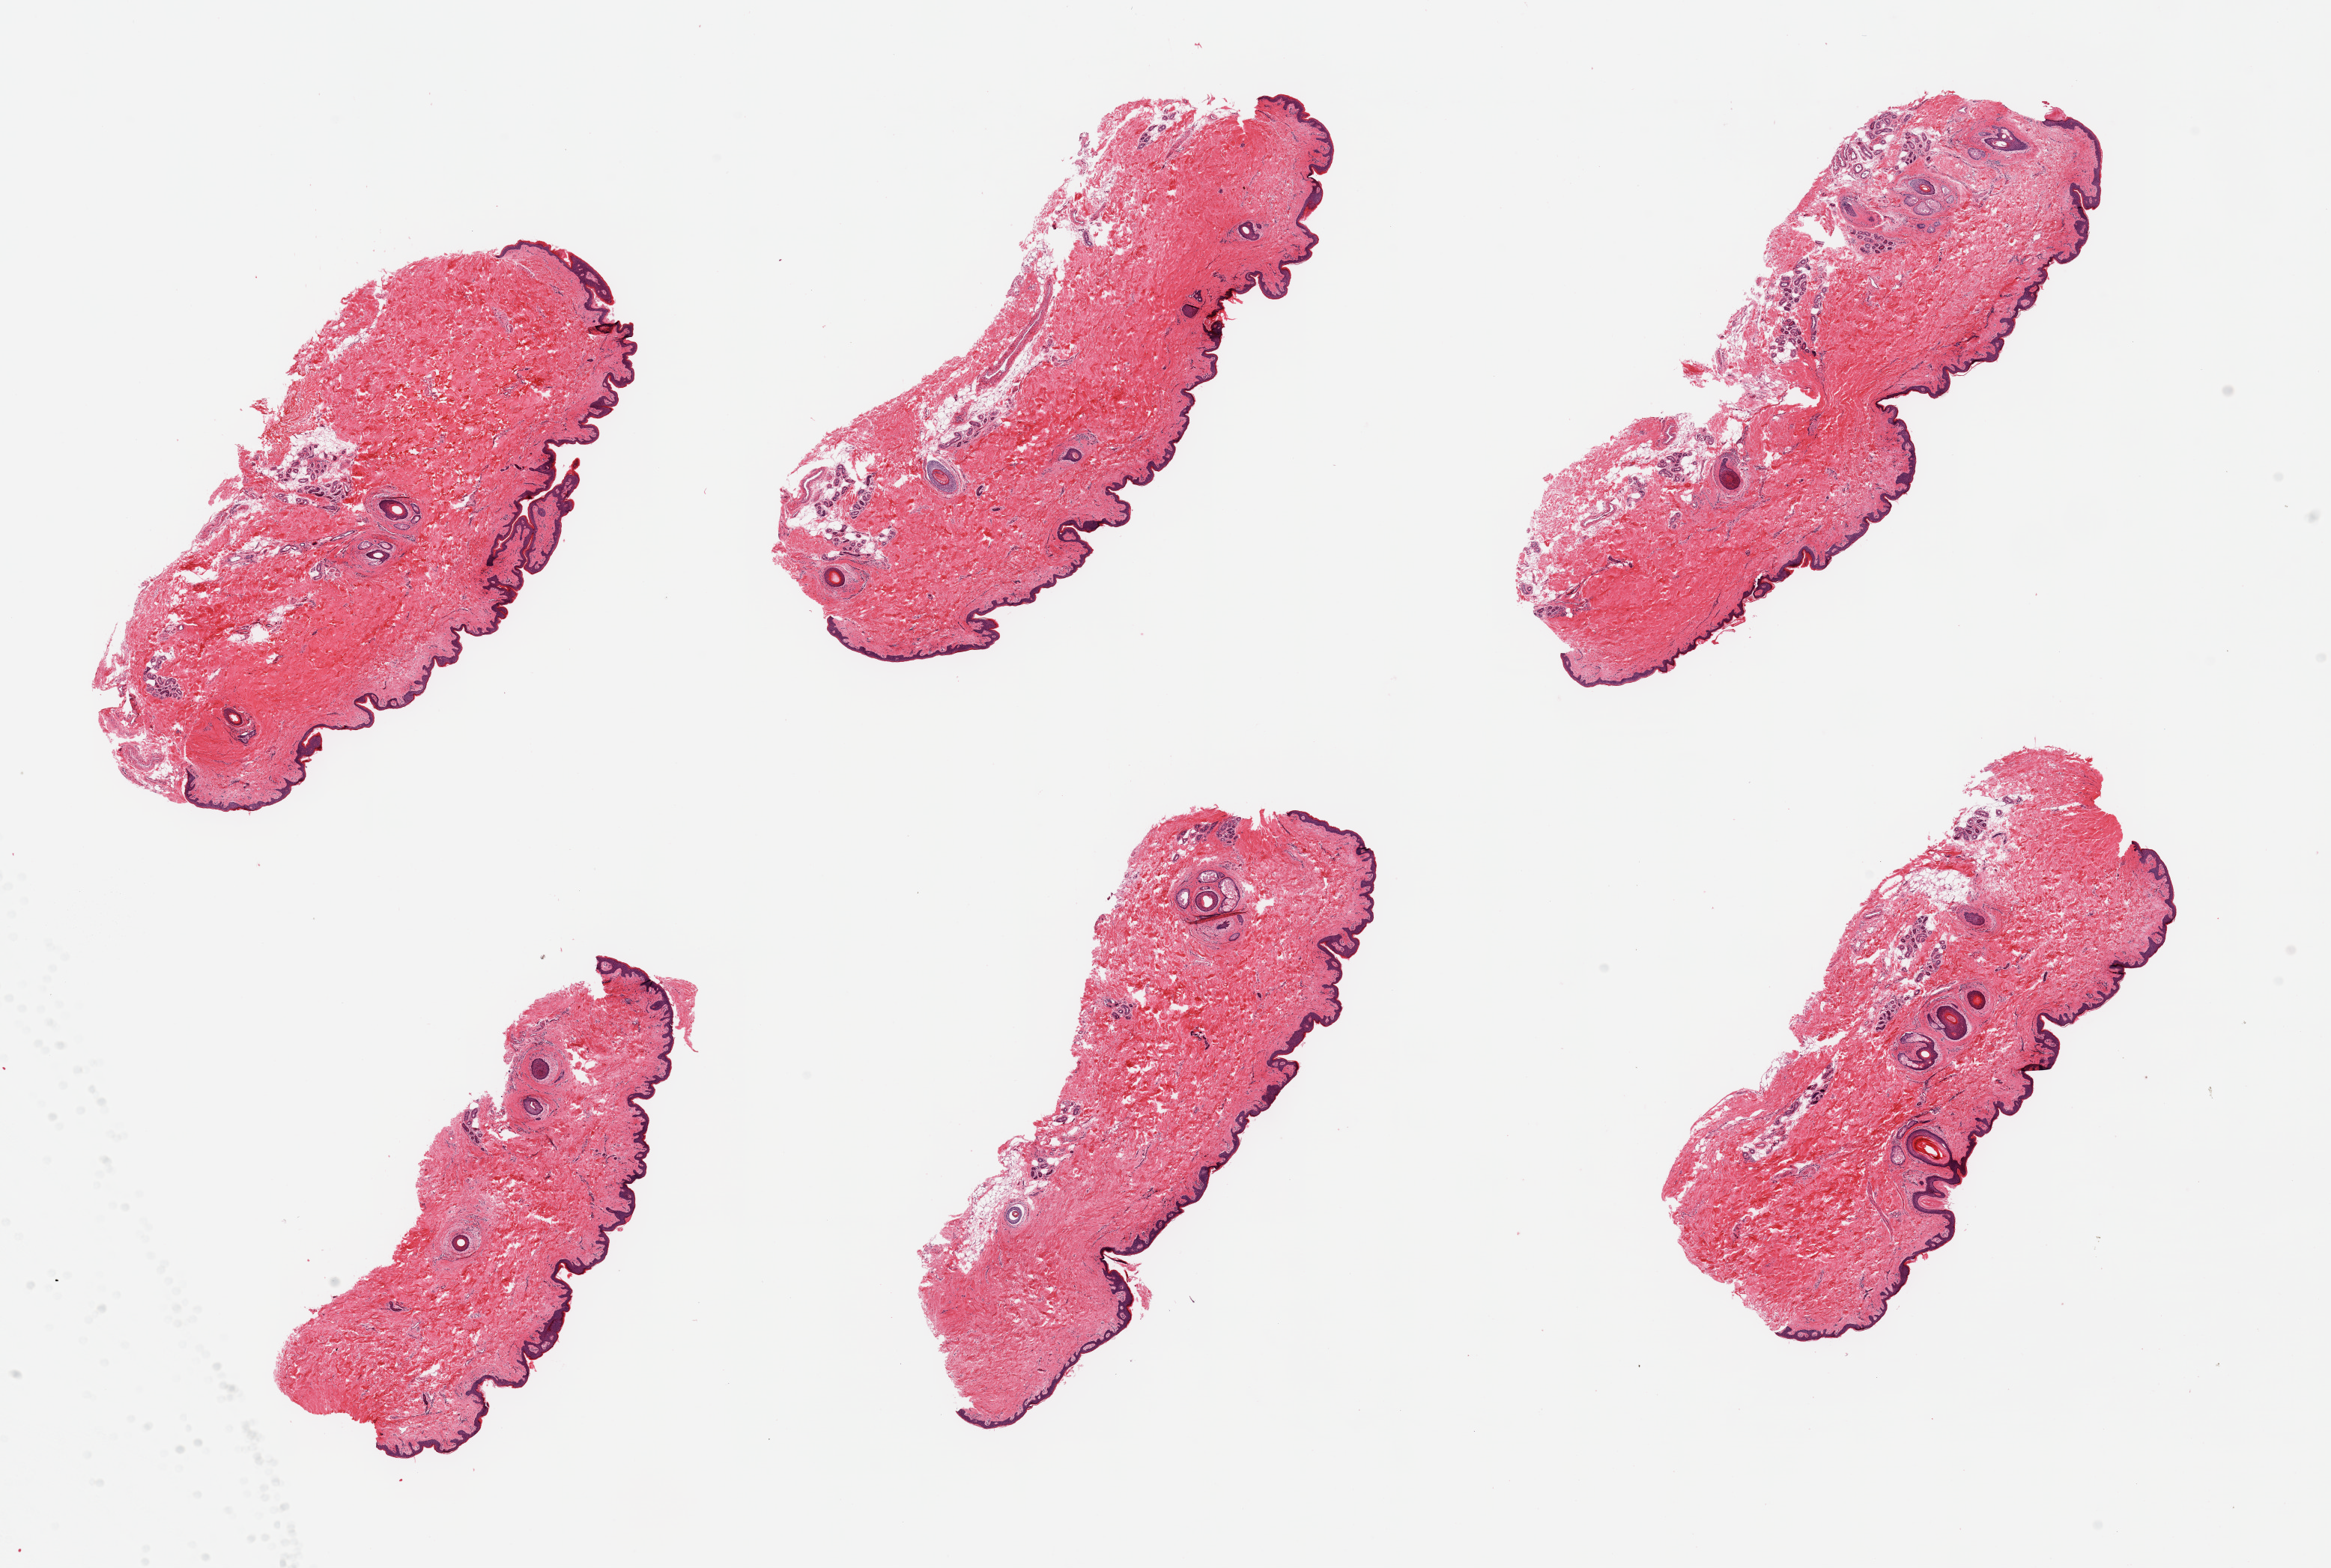
Whole-slide image, H&E stain, brightfield — a low-resolution overview of the entire scanned area, about 24.6 x 16.6 mm (slide scanned at 20x). PAXgene-fixed paraffin-embedded (PFPE) section. Section of skin of suprapubic region (target tissue). Donor tissue sample.
Reviewer comment on this tissue sample: 6 pieces; well trimmed with minimal internal fat.